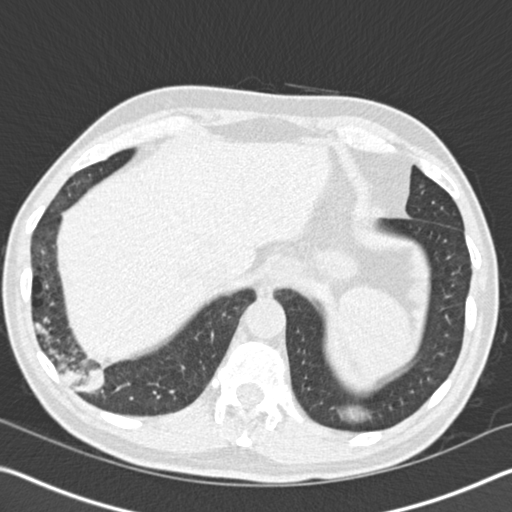
Chest CT (low-dose screening protocol), one axial image. Baseline annual screen. Lung window (W 1500 / L -600 HU). Slice 128 of 161 in the series. 512 × 512 image matrix. Male participant, aged 61 years at enrolment.
Expert-annotated lung lesion, bounding box <6,268,135,412> (left, top, right, bottom; pixels). Screening reader's record for this exam (one nodule recorded; not confirmed to be the boxed lesion): non-calcified nodule or mass ≥4 mm, right lower lobe, 52 × 36 mm, spiculated (stellate) margins, soft tissue attenuation. Participant outcome: lung cancer diagnosed 392 days after this screen — bronchiolo-alveolar adenocarcinoma, NOS, right lower lobe, moderately differentiated (G2), stage IIIB (AJCC 6th edition), 90 mm at pathology.